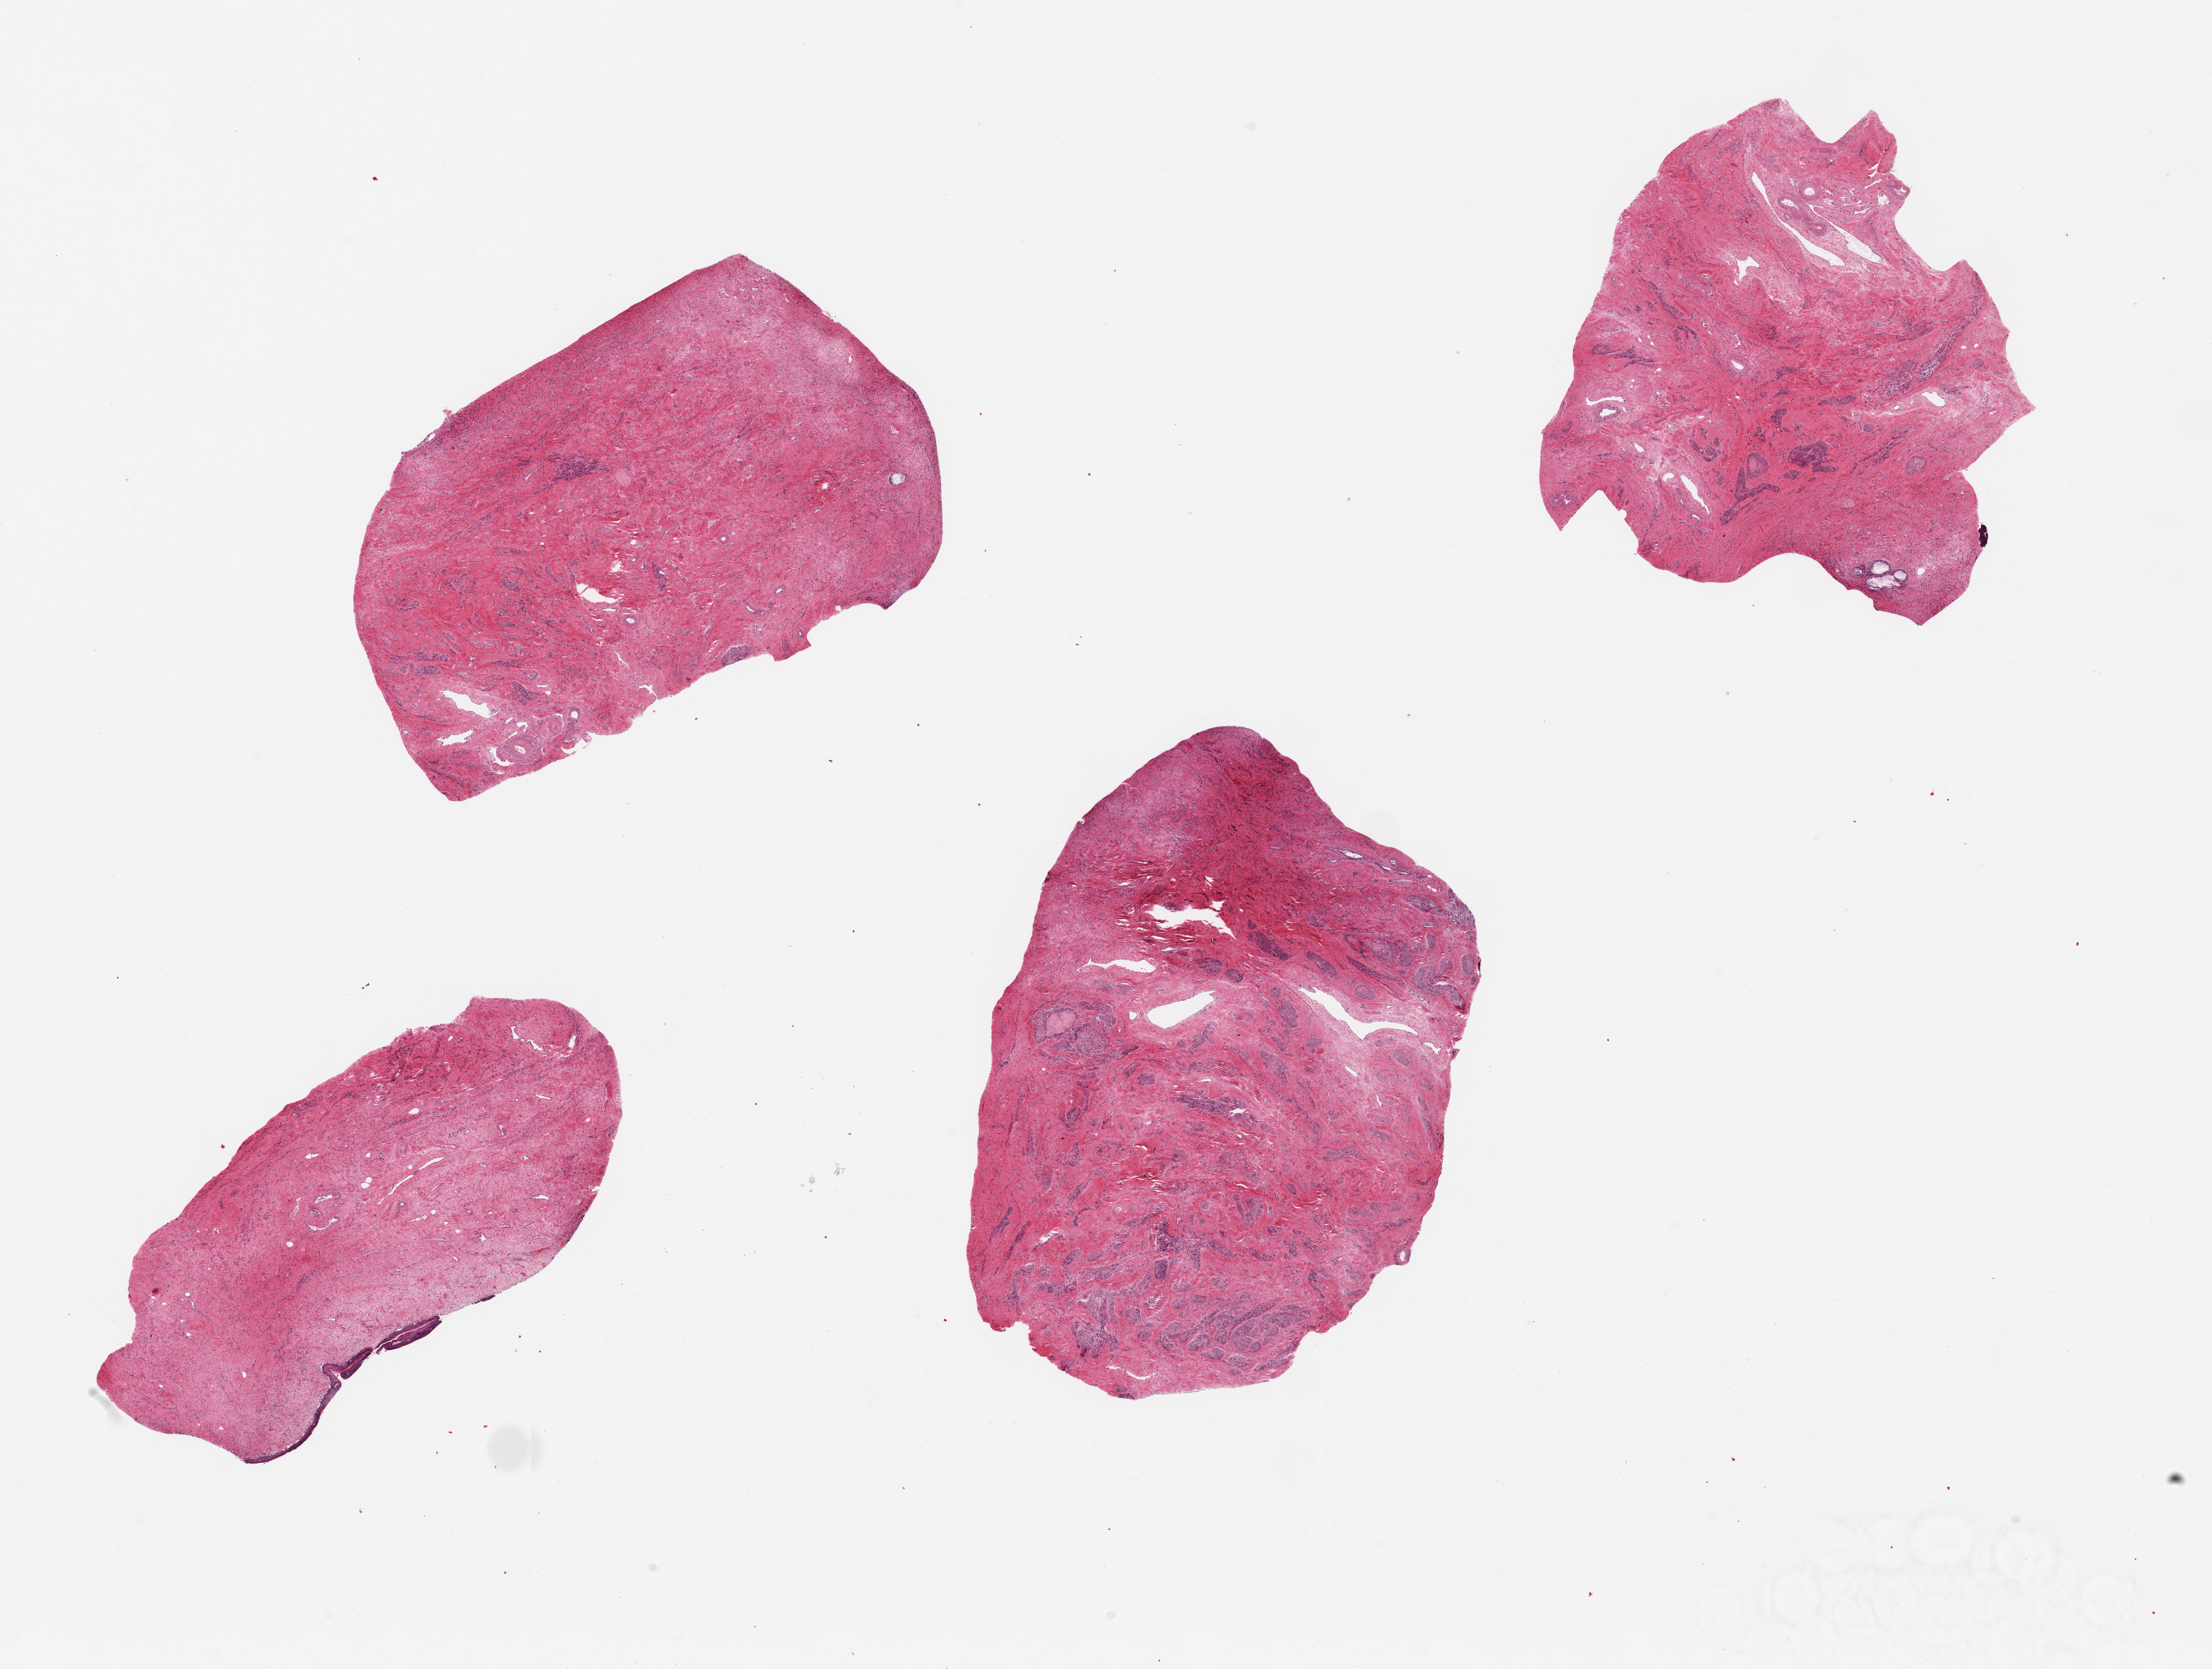
Haematoxylin and eosin whole-slide image, shown as a low-resolution overview of the whole scanned area (about 24.6 x 18.6 mm), PAXgene-fixed paraffin-embedded (PFPE) section, target tissue: endocervix, tissue donor sample. Donor: female.
* reviewer comment on this tissue sample: 4 pieces up to 6.7x5 mm; 1 piece is endocervix, 1 is ectocervix (images labelled), 2 are without epithelium